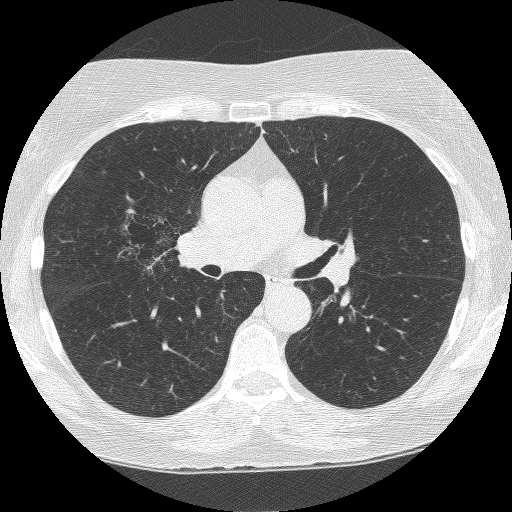
Axial slice from a low-dose chest CT screening exam, second screening round (one year after baseline), lung window (W 1500 / L -600 HU), lung (sharp) reconstruction kernel (BONE), 120 kVp, 512 × 512 image matrix, field of view 308 × 308 mm. Female participant, aged 64 years at enrolment. Former smoker at enrolment.
Lesion marked by an expert reader, bounding box [x1, y1, x2, y2] px = [116, 206, 201, 287]. The screening reader recorded 4 non-calcified nodules or masses ≥4 mm on this exam (right upper lobe, right upper lobe, right upper lobe, left upper lobe); which of them this box marks is not recorded. Official screen result: positive, other. Participant outcome: lung cancer diagnosed 381 days after this screen (after the third annual screen) — adenocarcinoma, NOS, right upper lobe, right middle lobe, right hilum, stage IV (AJCC 6th edition), 85 mm at pathology.